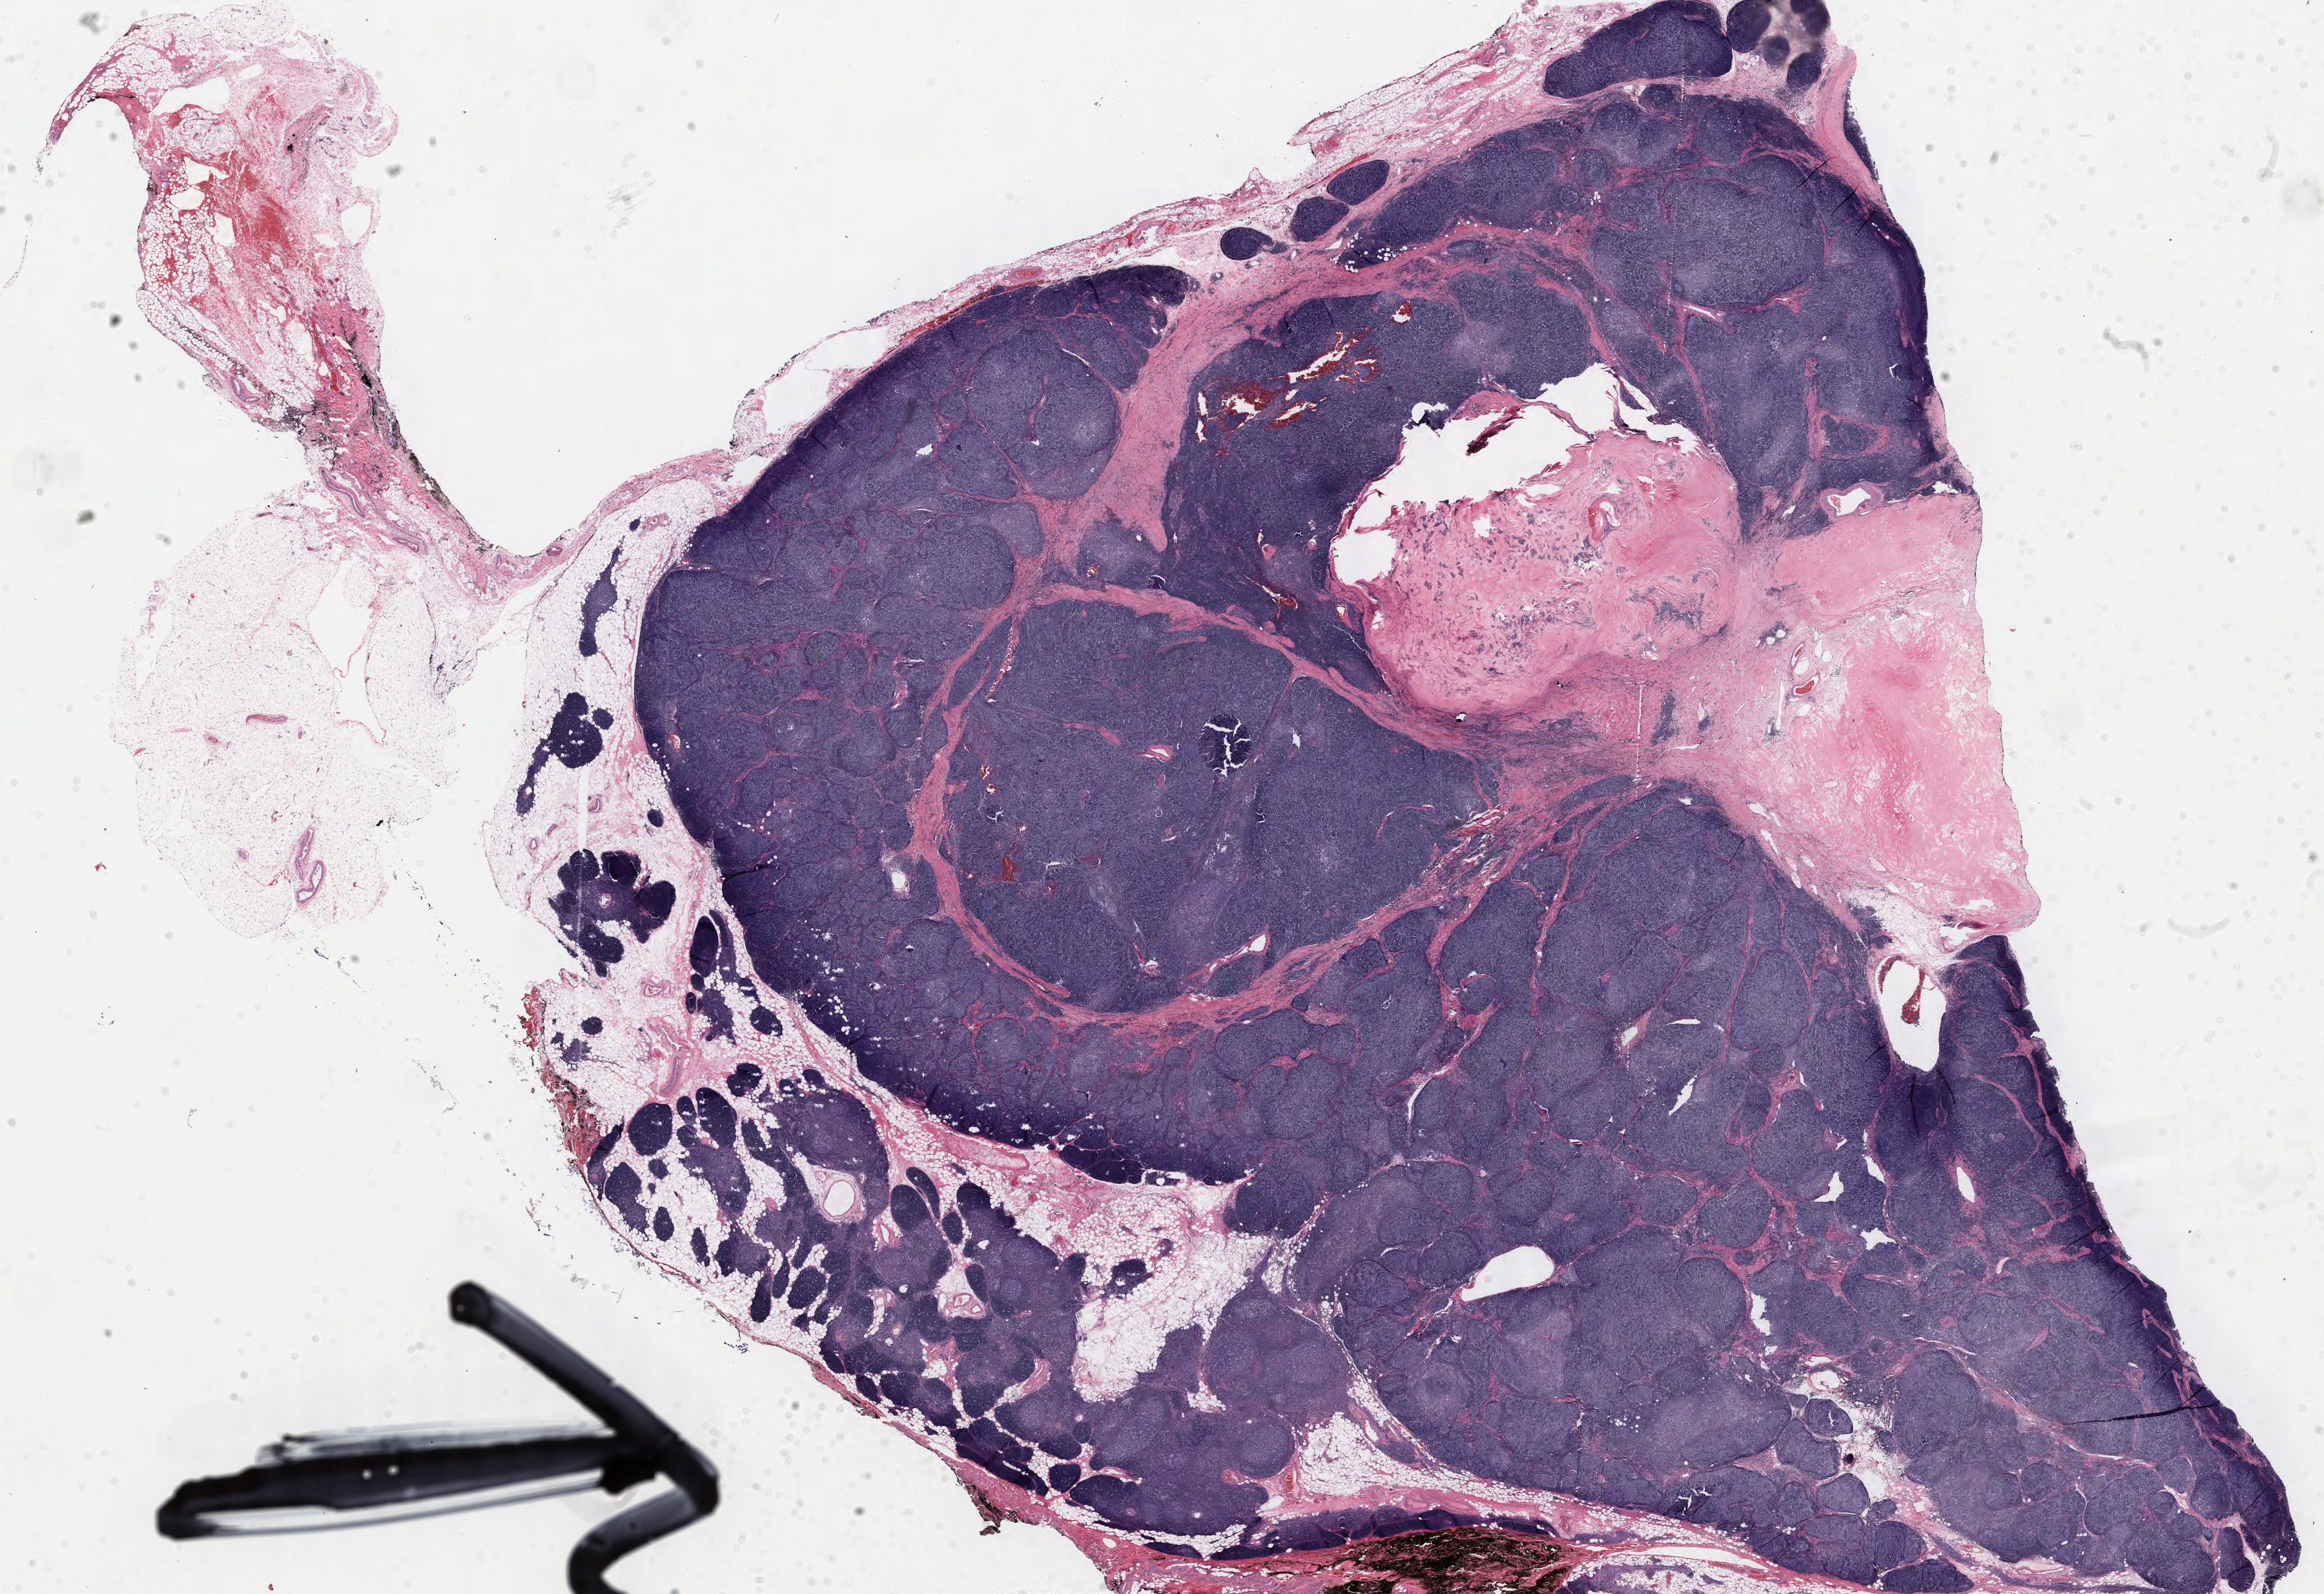
Digitized H&E tissue section (whole slide), low-resolution overview of the scanned area, about 28.5 x 19.6 mm; formalin-fixed paraffin-embedded (FFPE) diagnostic section; sample: primary tumour, thymus. Patient: male, age at initial diagnosis 44 years.
Histologic diagnosis: Thymoma, type B2, malignant.